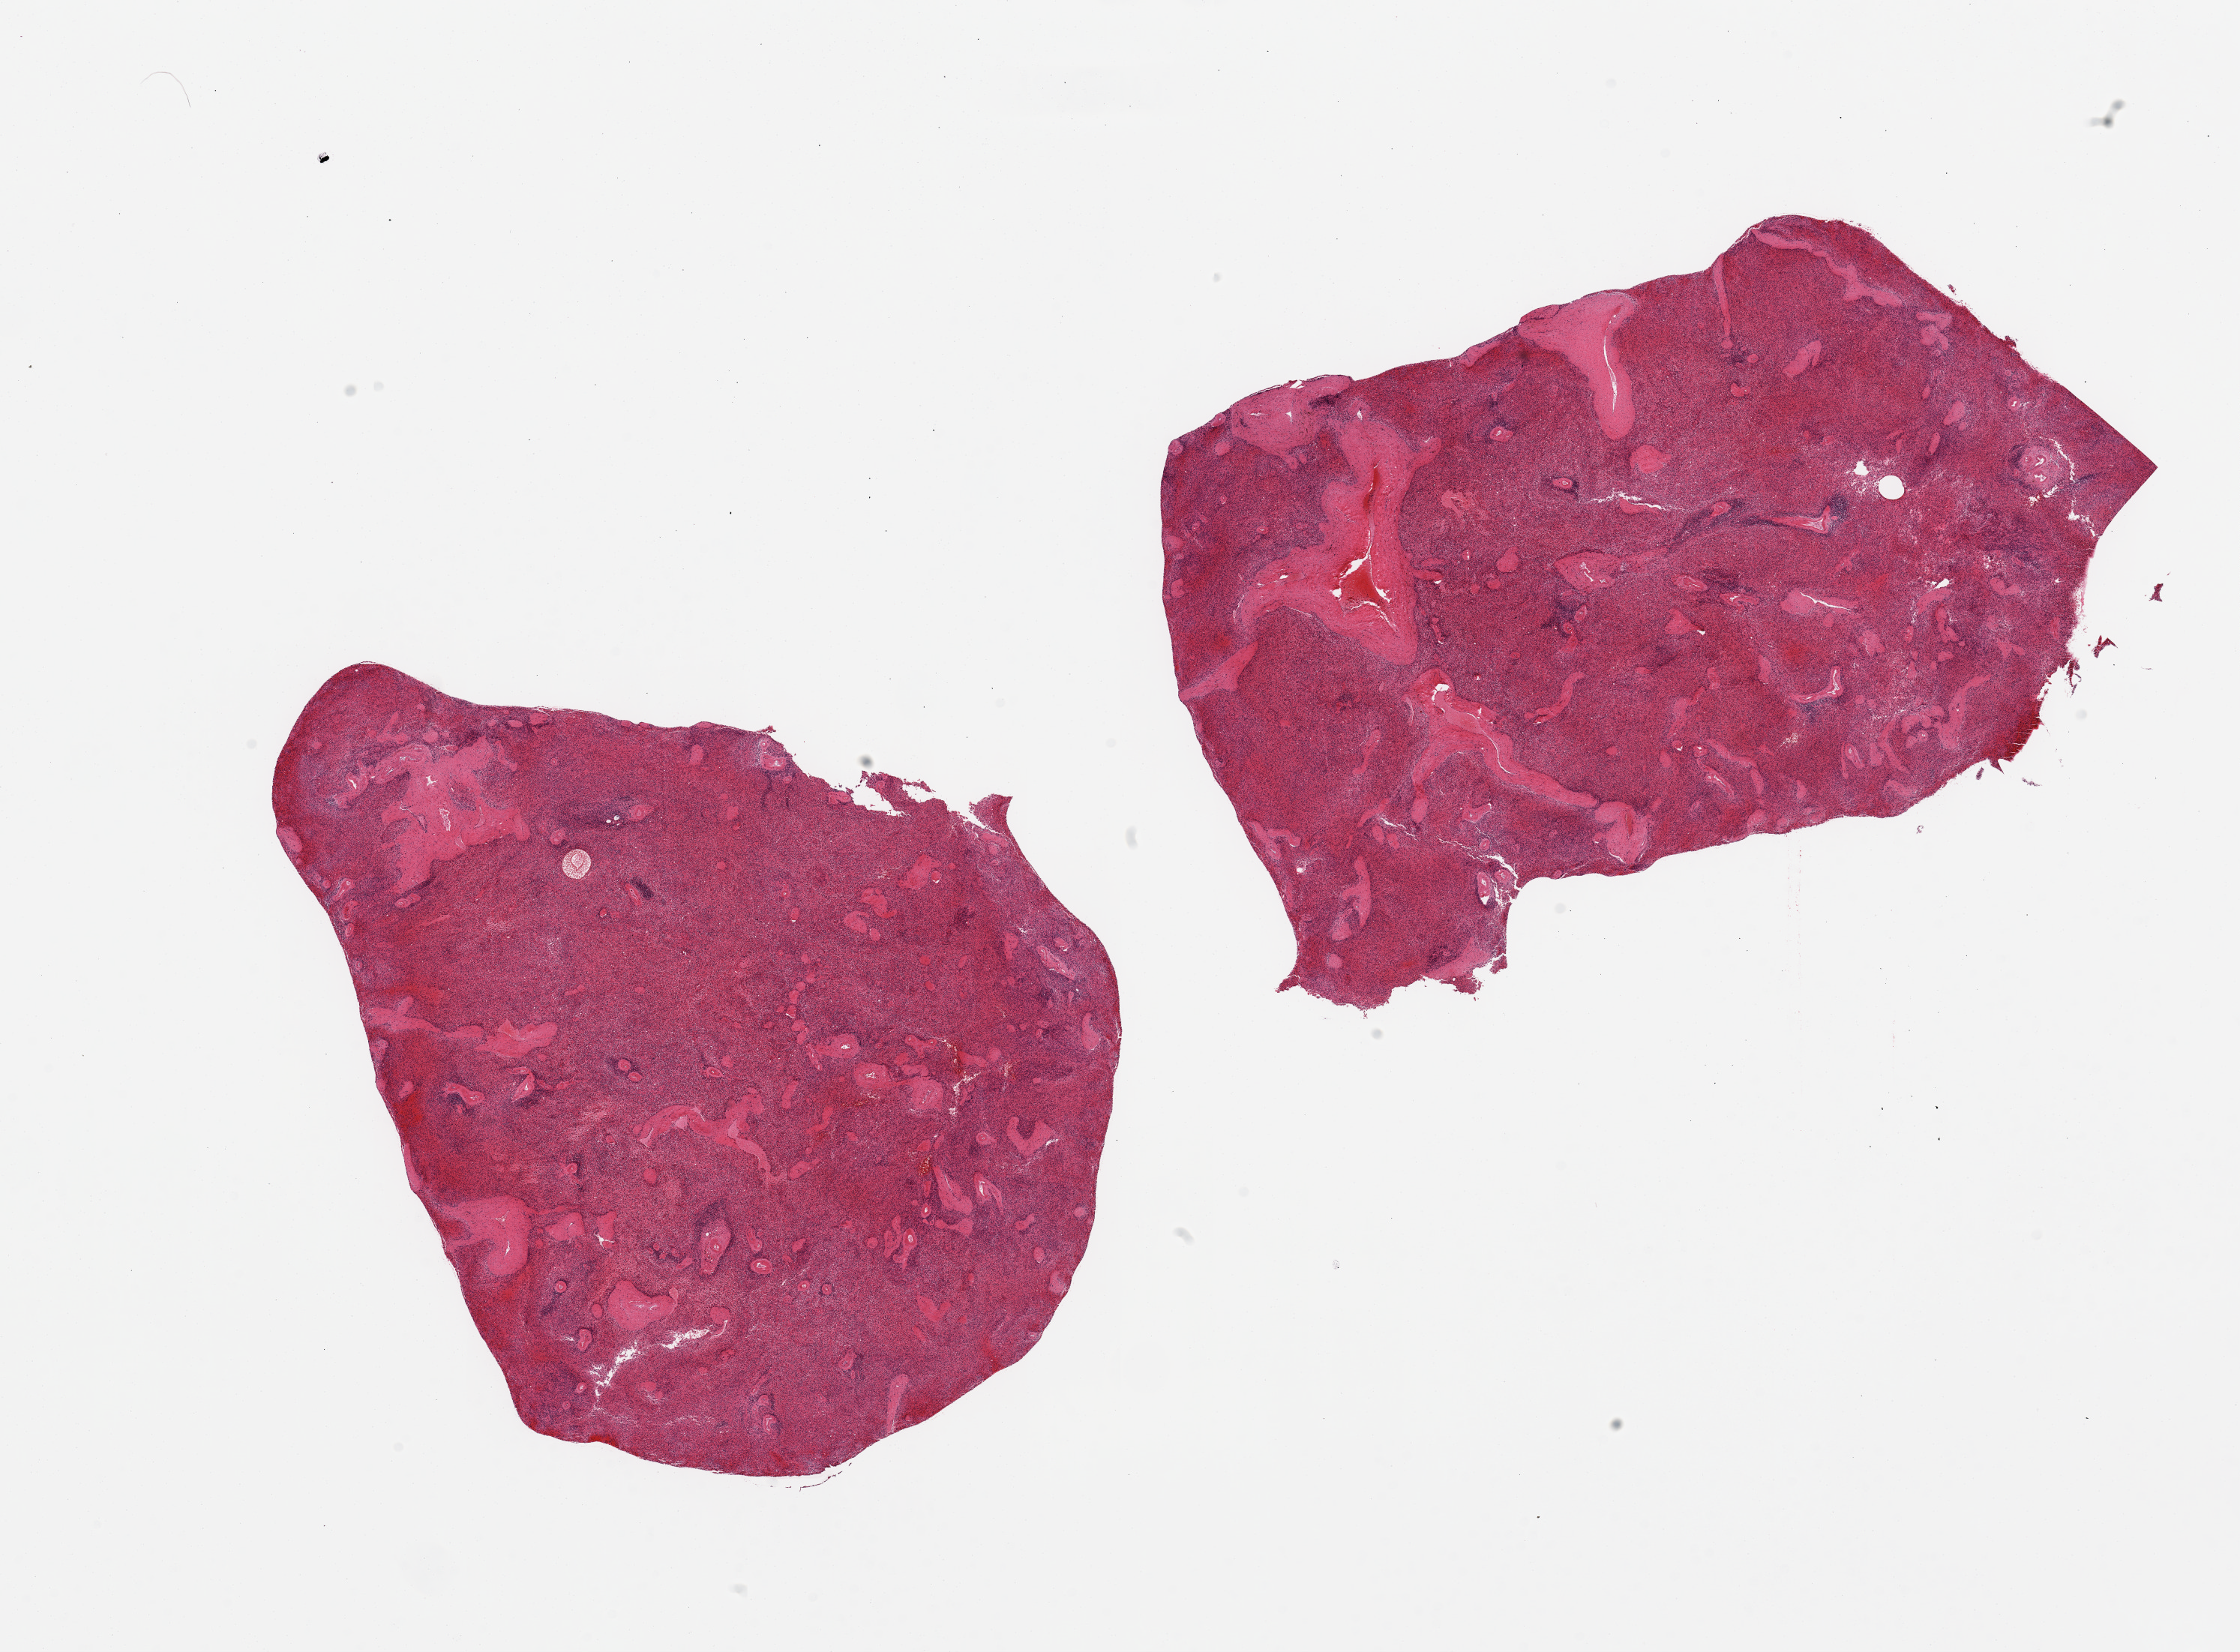
Digitized haematoxylin and eosin-stained section — a low-resolution overview of the entire scanned area, about 23.6 x 17.4 mm, PAXgene-fixed paraffin-embedded (PFPE) section, section of spleen (target tissue), donor tissue sample.
Pathologist's review note for this sample: 2 pieces; mild congestion.